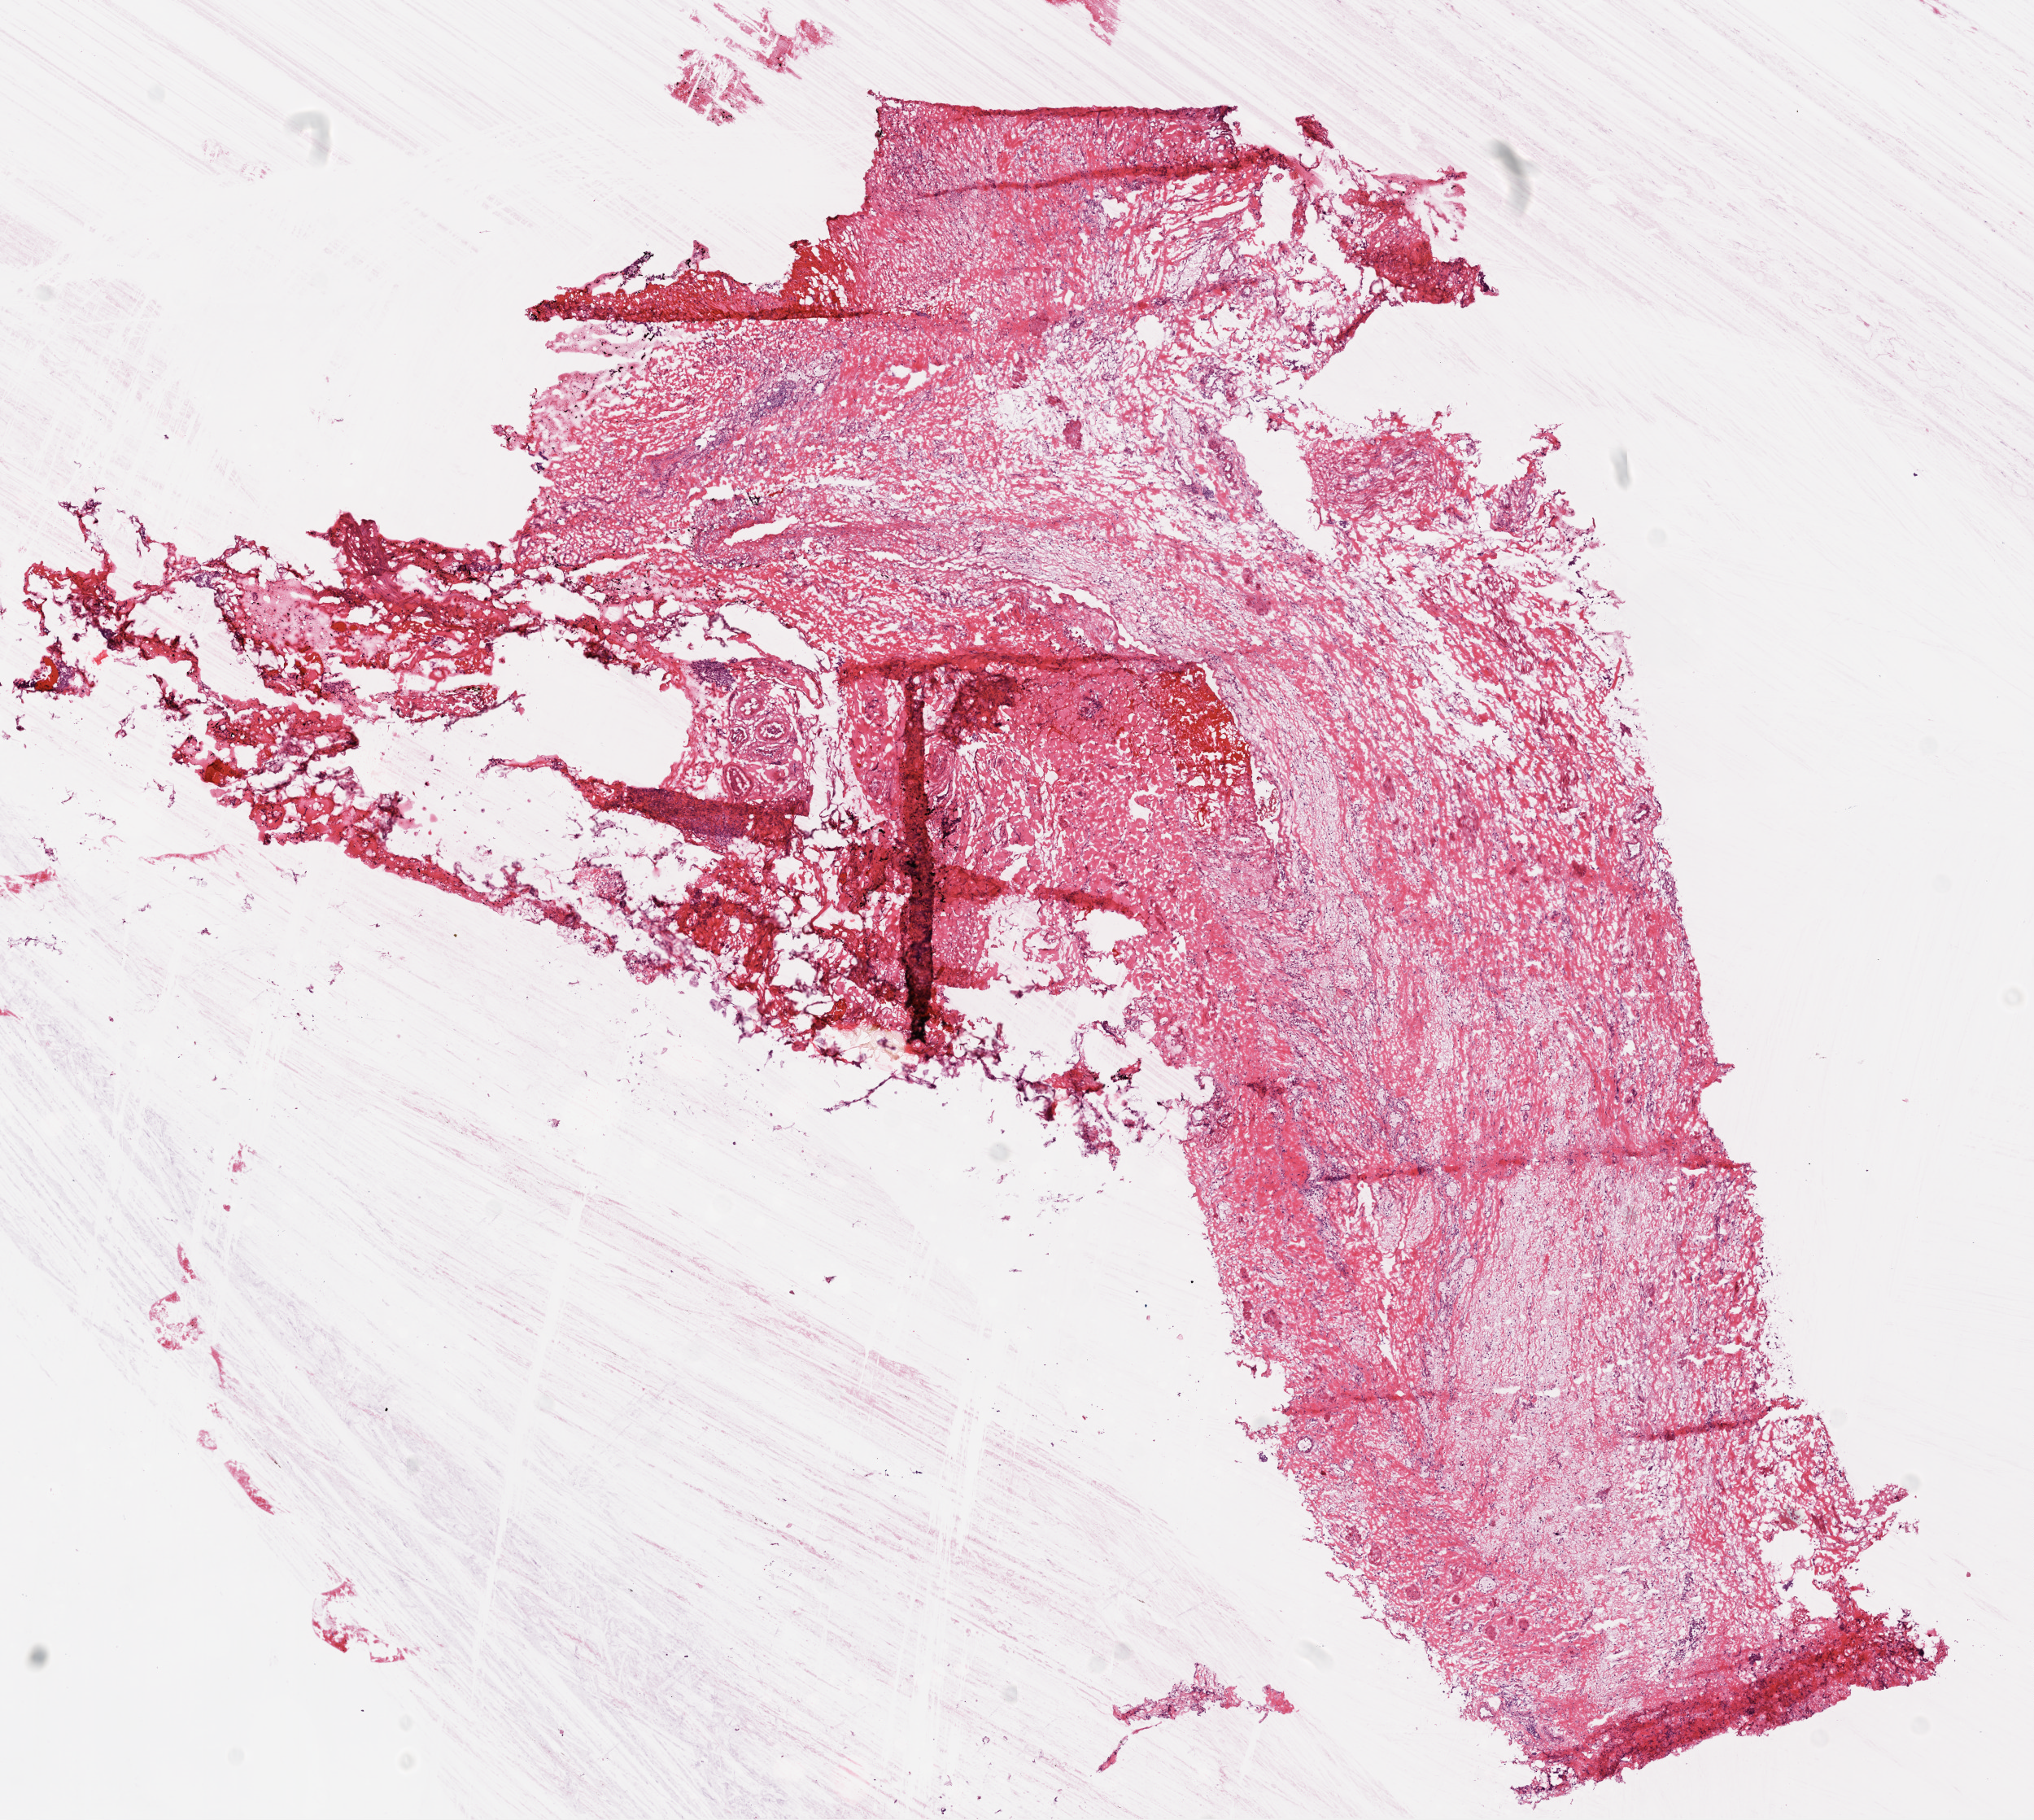
H&E whole-slide image — whole scanned area (about 10.0 x 9.0 mm, acquisition: 20x scan) shown as a low-resolution overview; frozen section from the top of the tissue portion; solid tissue normal (non-tumour tissue) sample from the ovary. Female, age 66 years at initial diagnosis.
- this section: solid tissue normal sample (biorepository sample class)
- patient diagnosis: Serous cystadenocarcinoma, NOS